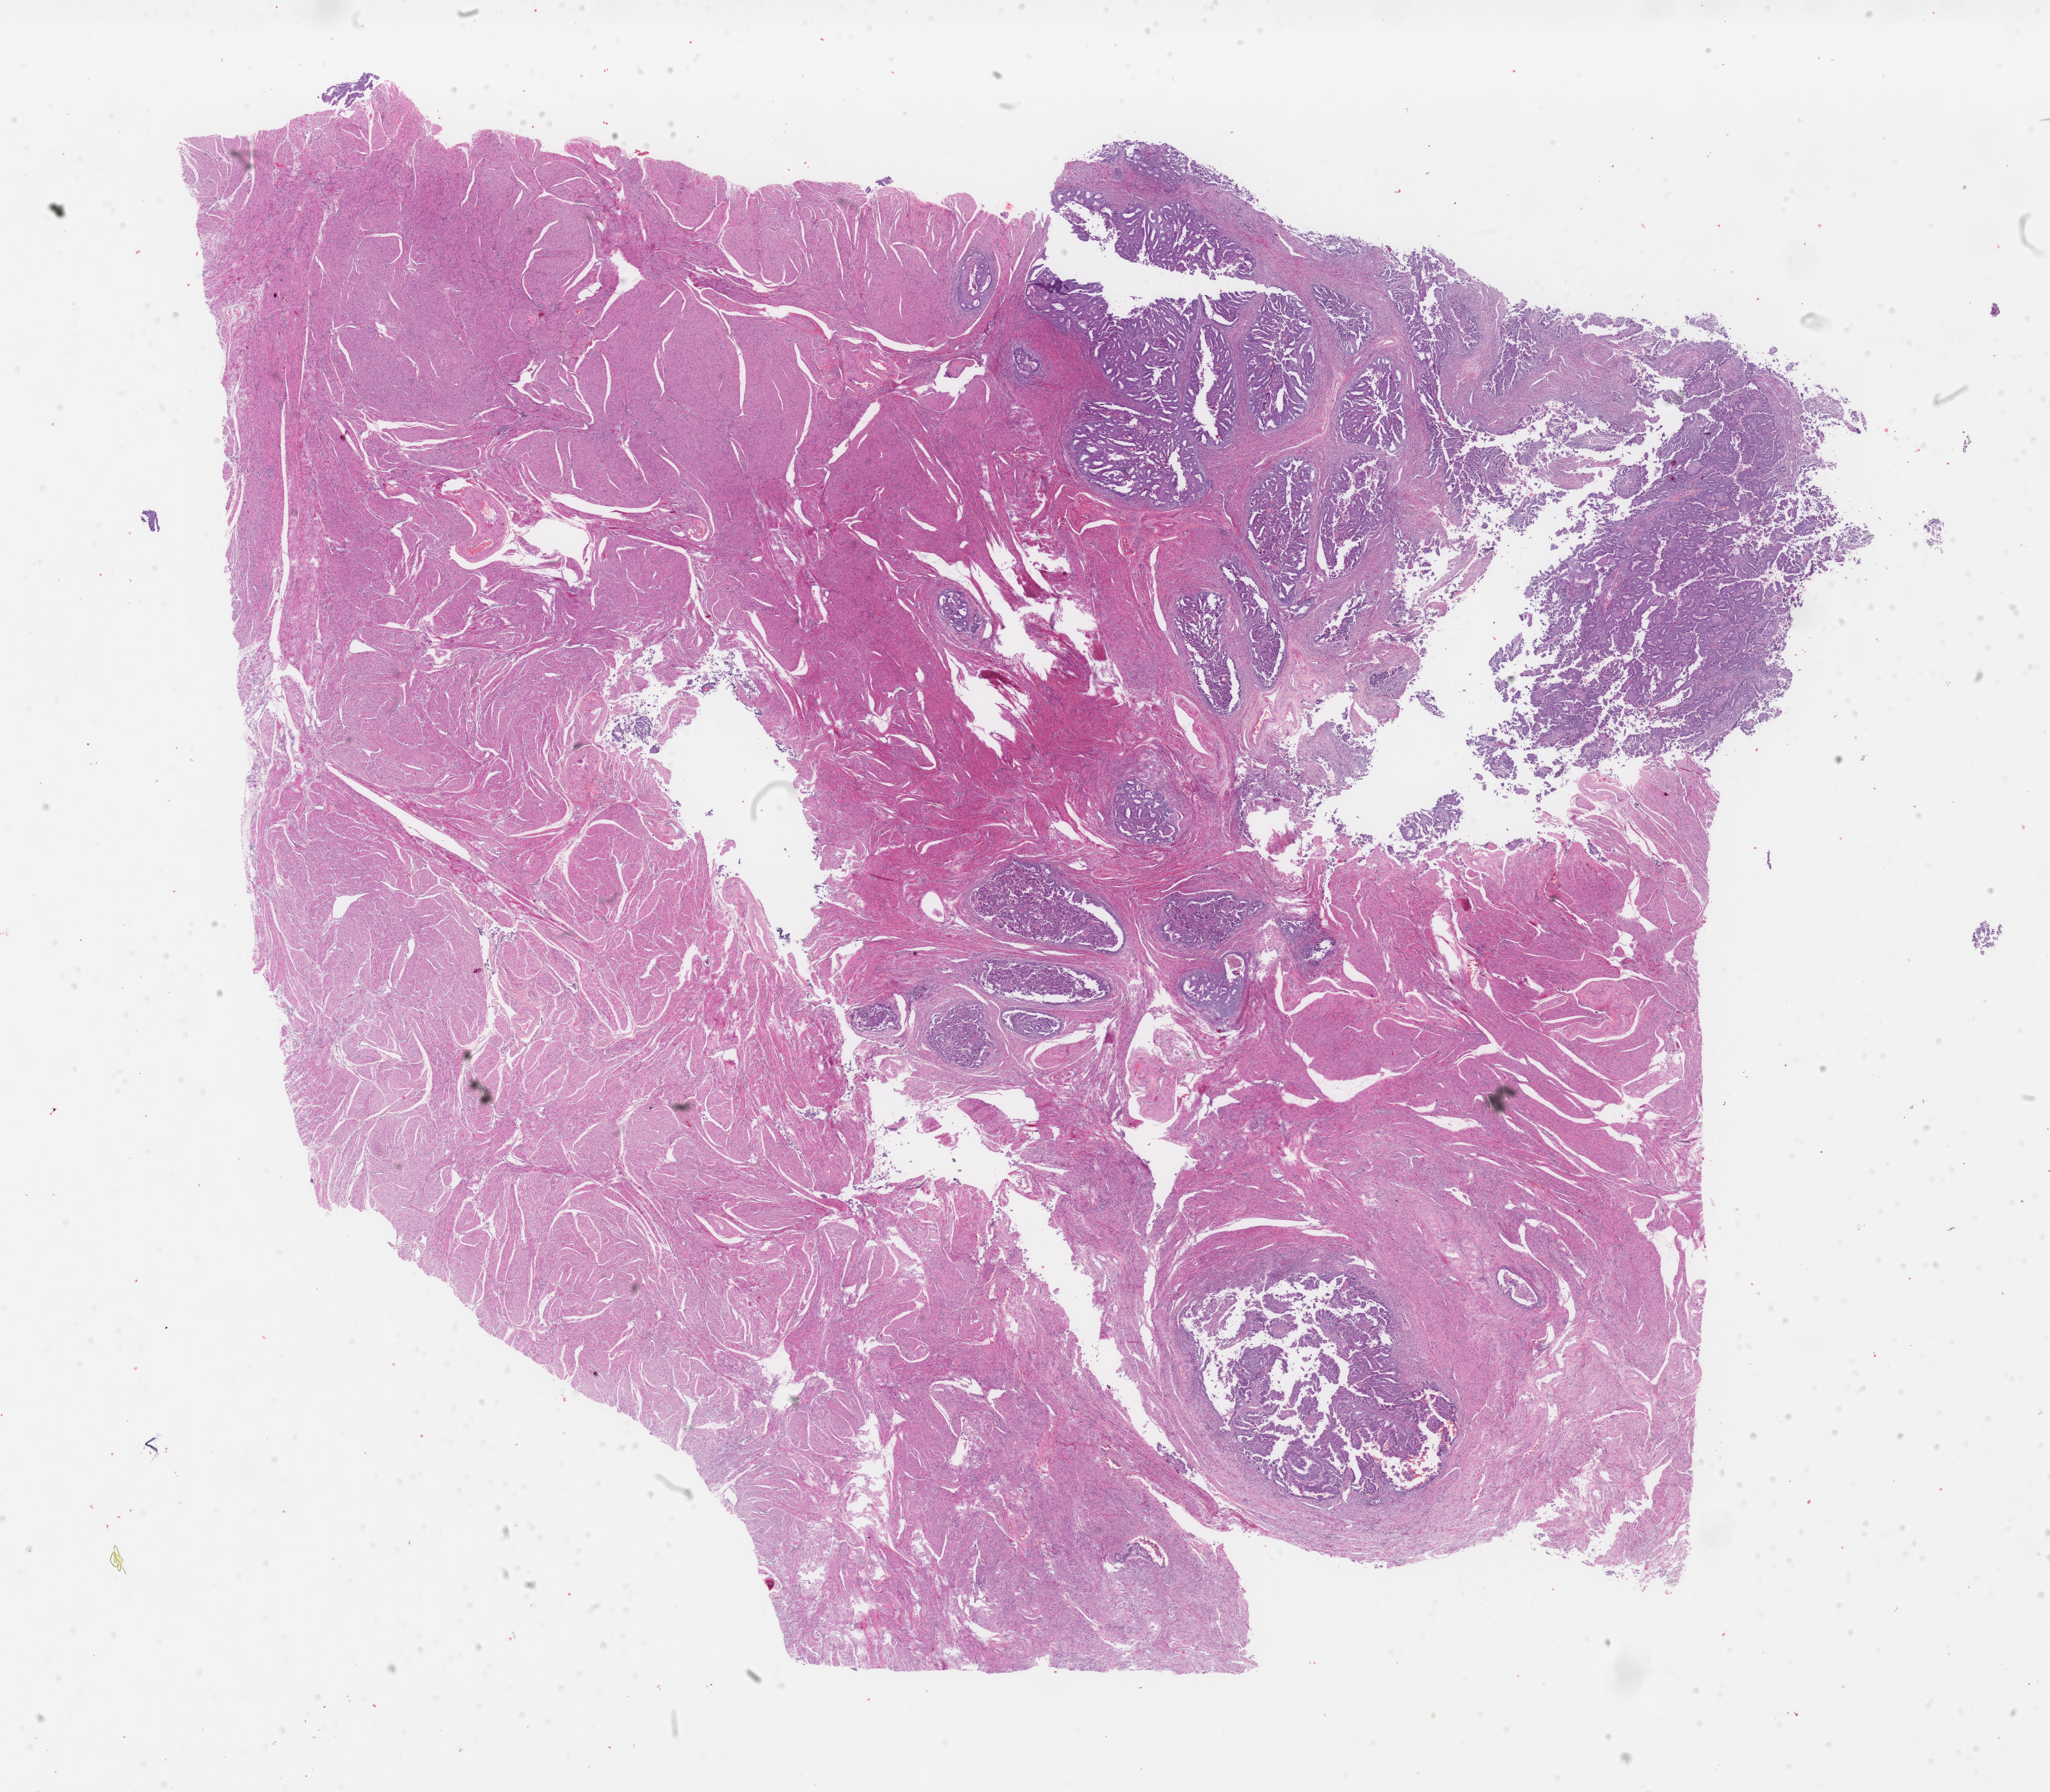
Whole-slide histology image, H&E — whole scanned area (about 25.3 x 22.1 mm) shown as a low-resolution overview; formalin-fixed paraffin-embedded (FFPE) diagnostic section; uterus, primary tumour sample. Patient: female, age at initial diagnosis 64 years. Histologic grade: G1 (well differentiated).
Pathologic diagnosis: Endometrioid adenocarcinoma, NOS. FIGO stage: IA.